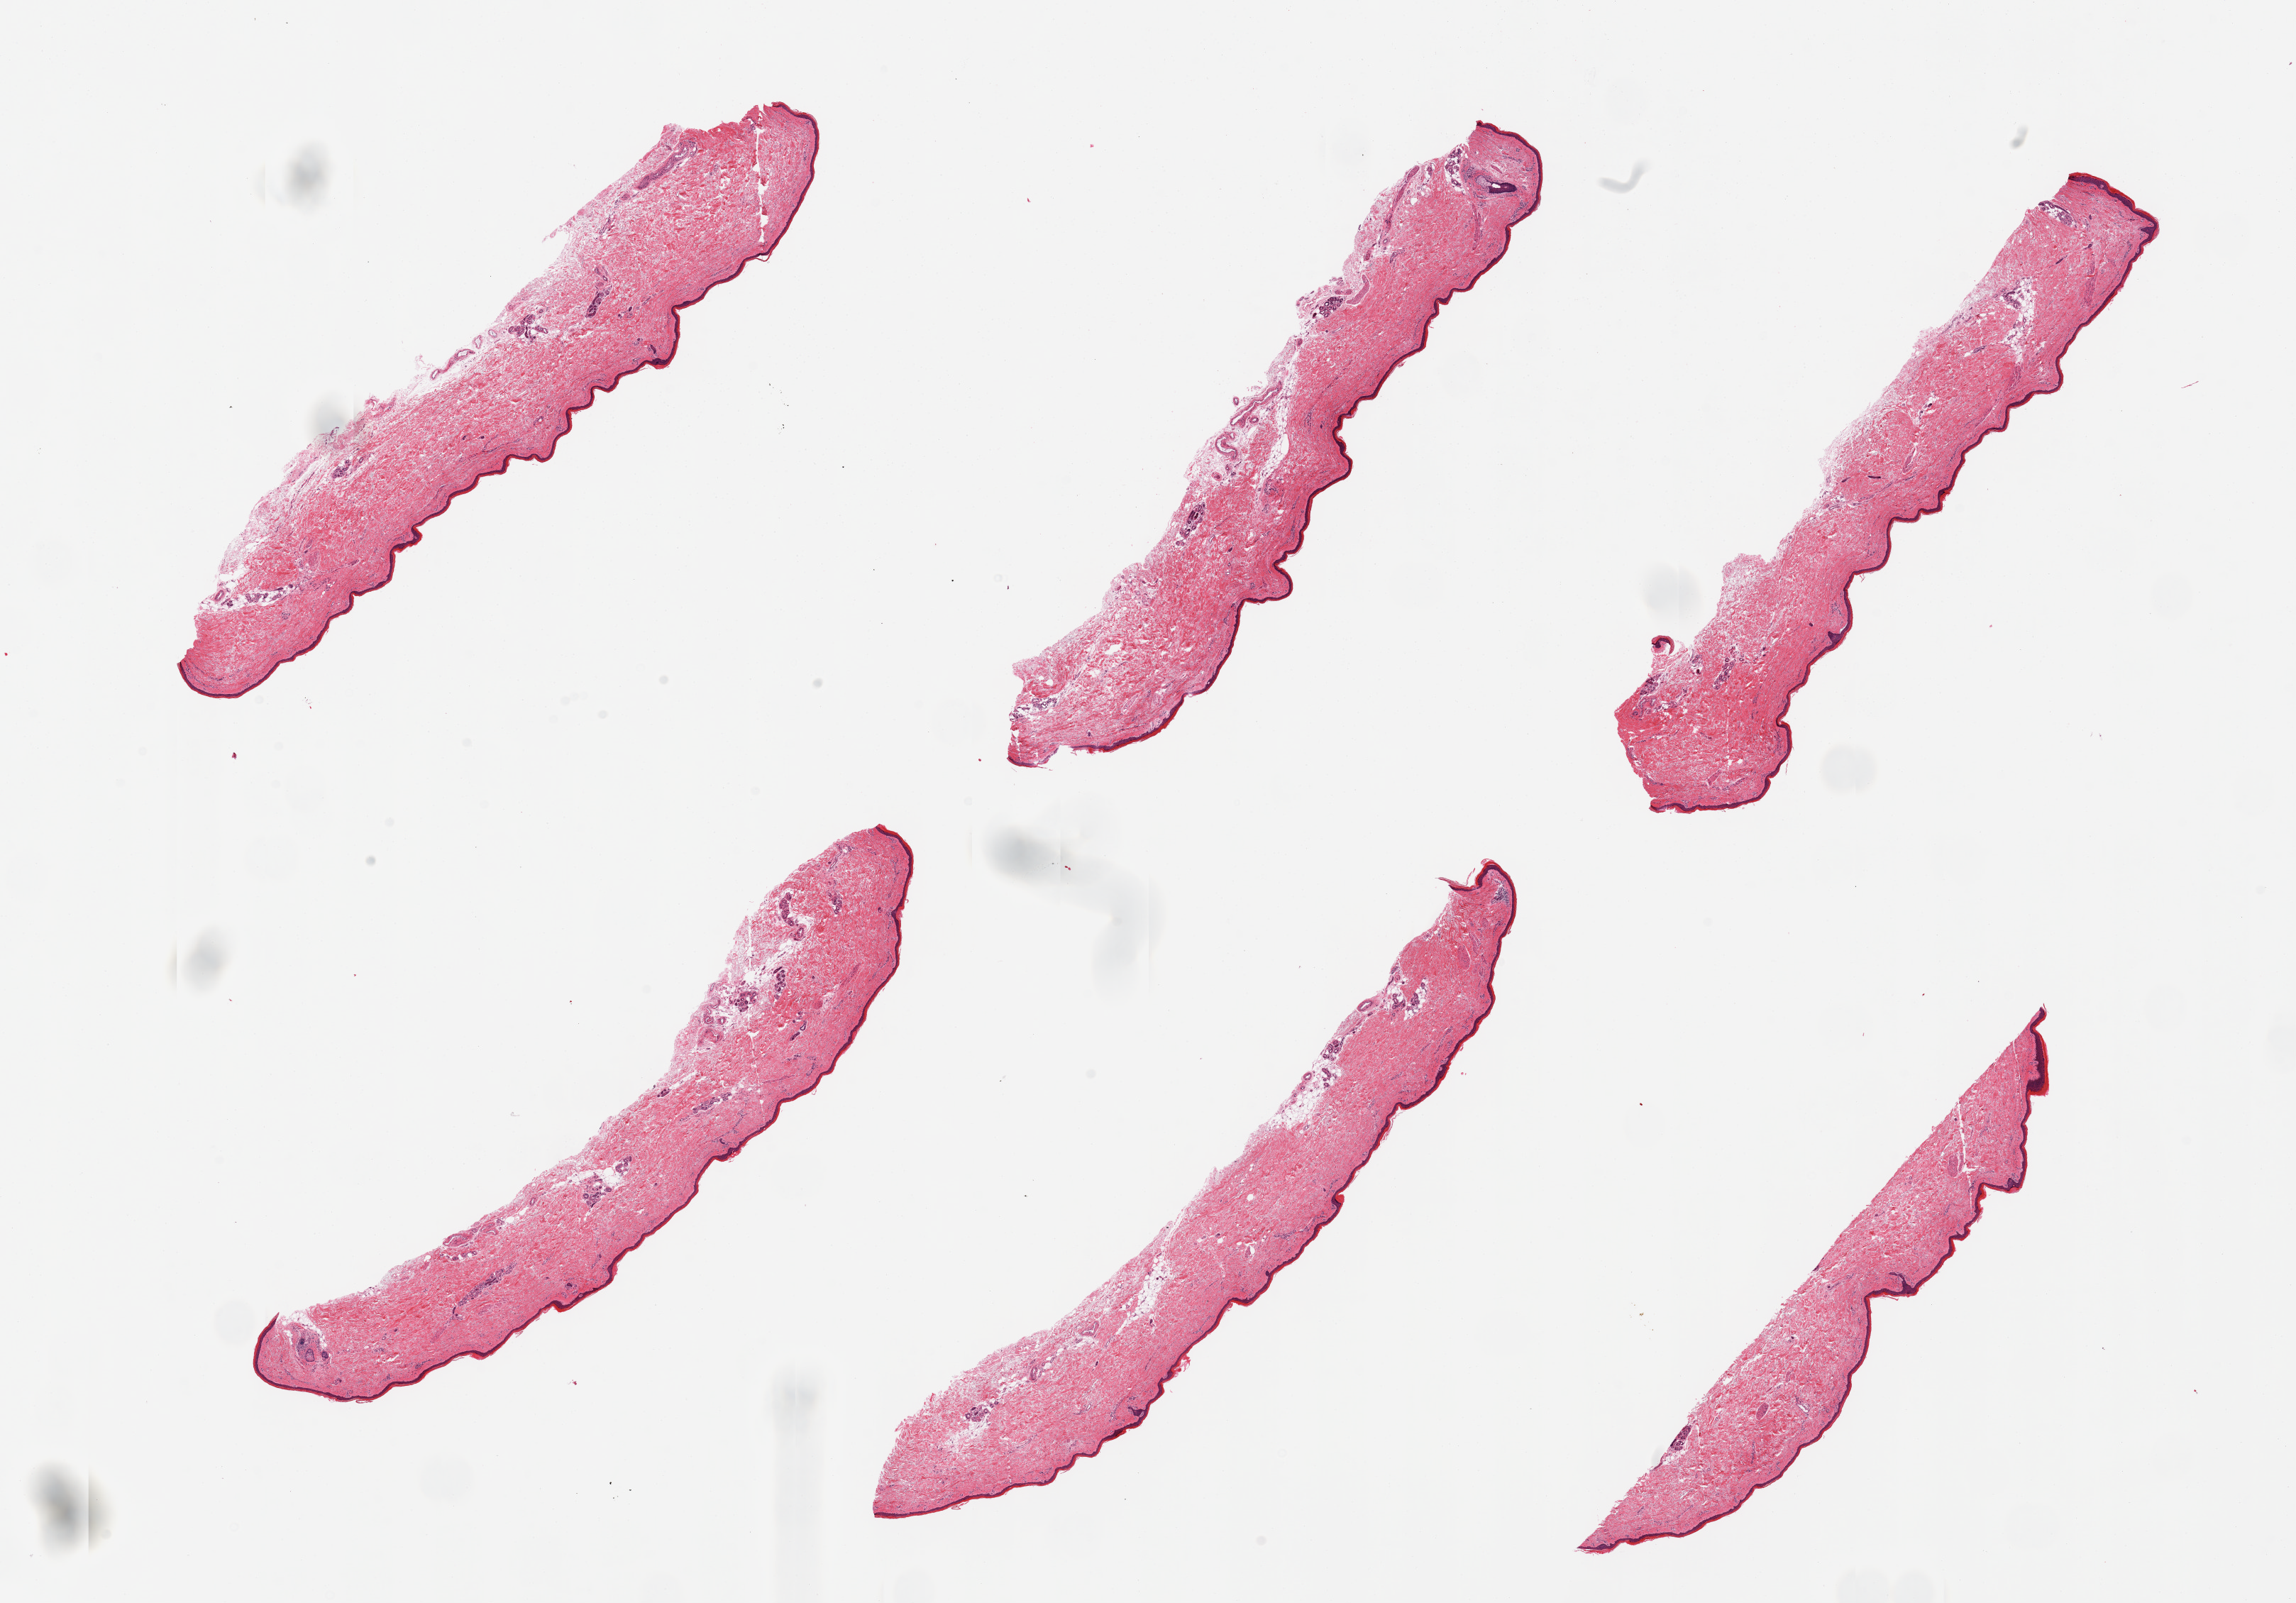
Whole-slide image, hematoxylin and eosin (H&E) stain, a low-resolution overview of the entire scanned area, about 25.6 x 17.9 mm; PAXgene-fixed, paraffin-embedded tissue; target tissue: skin of lower leg; donor tissue sample. Donor sex: female.
Reviewer comment on this tissue sample: 6 pieces; well trimmed.